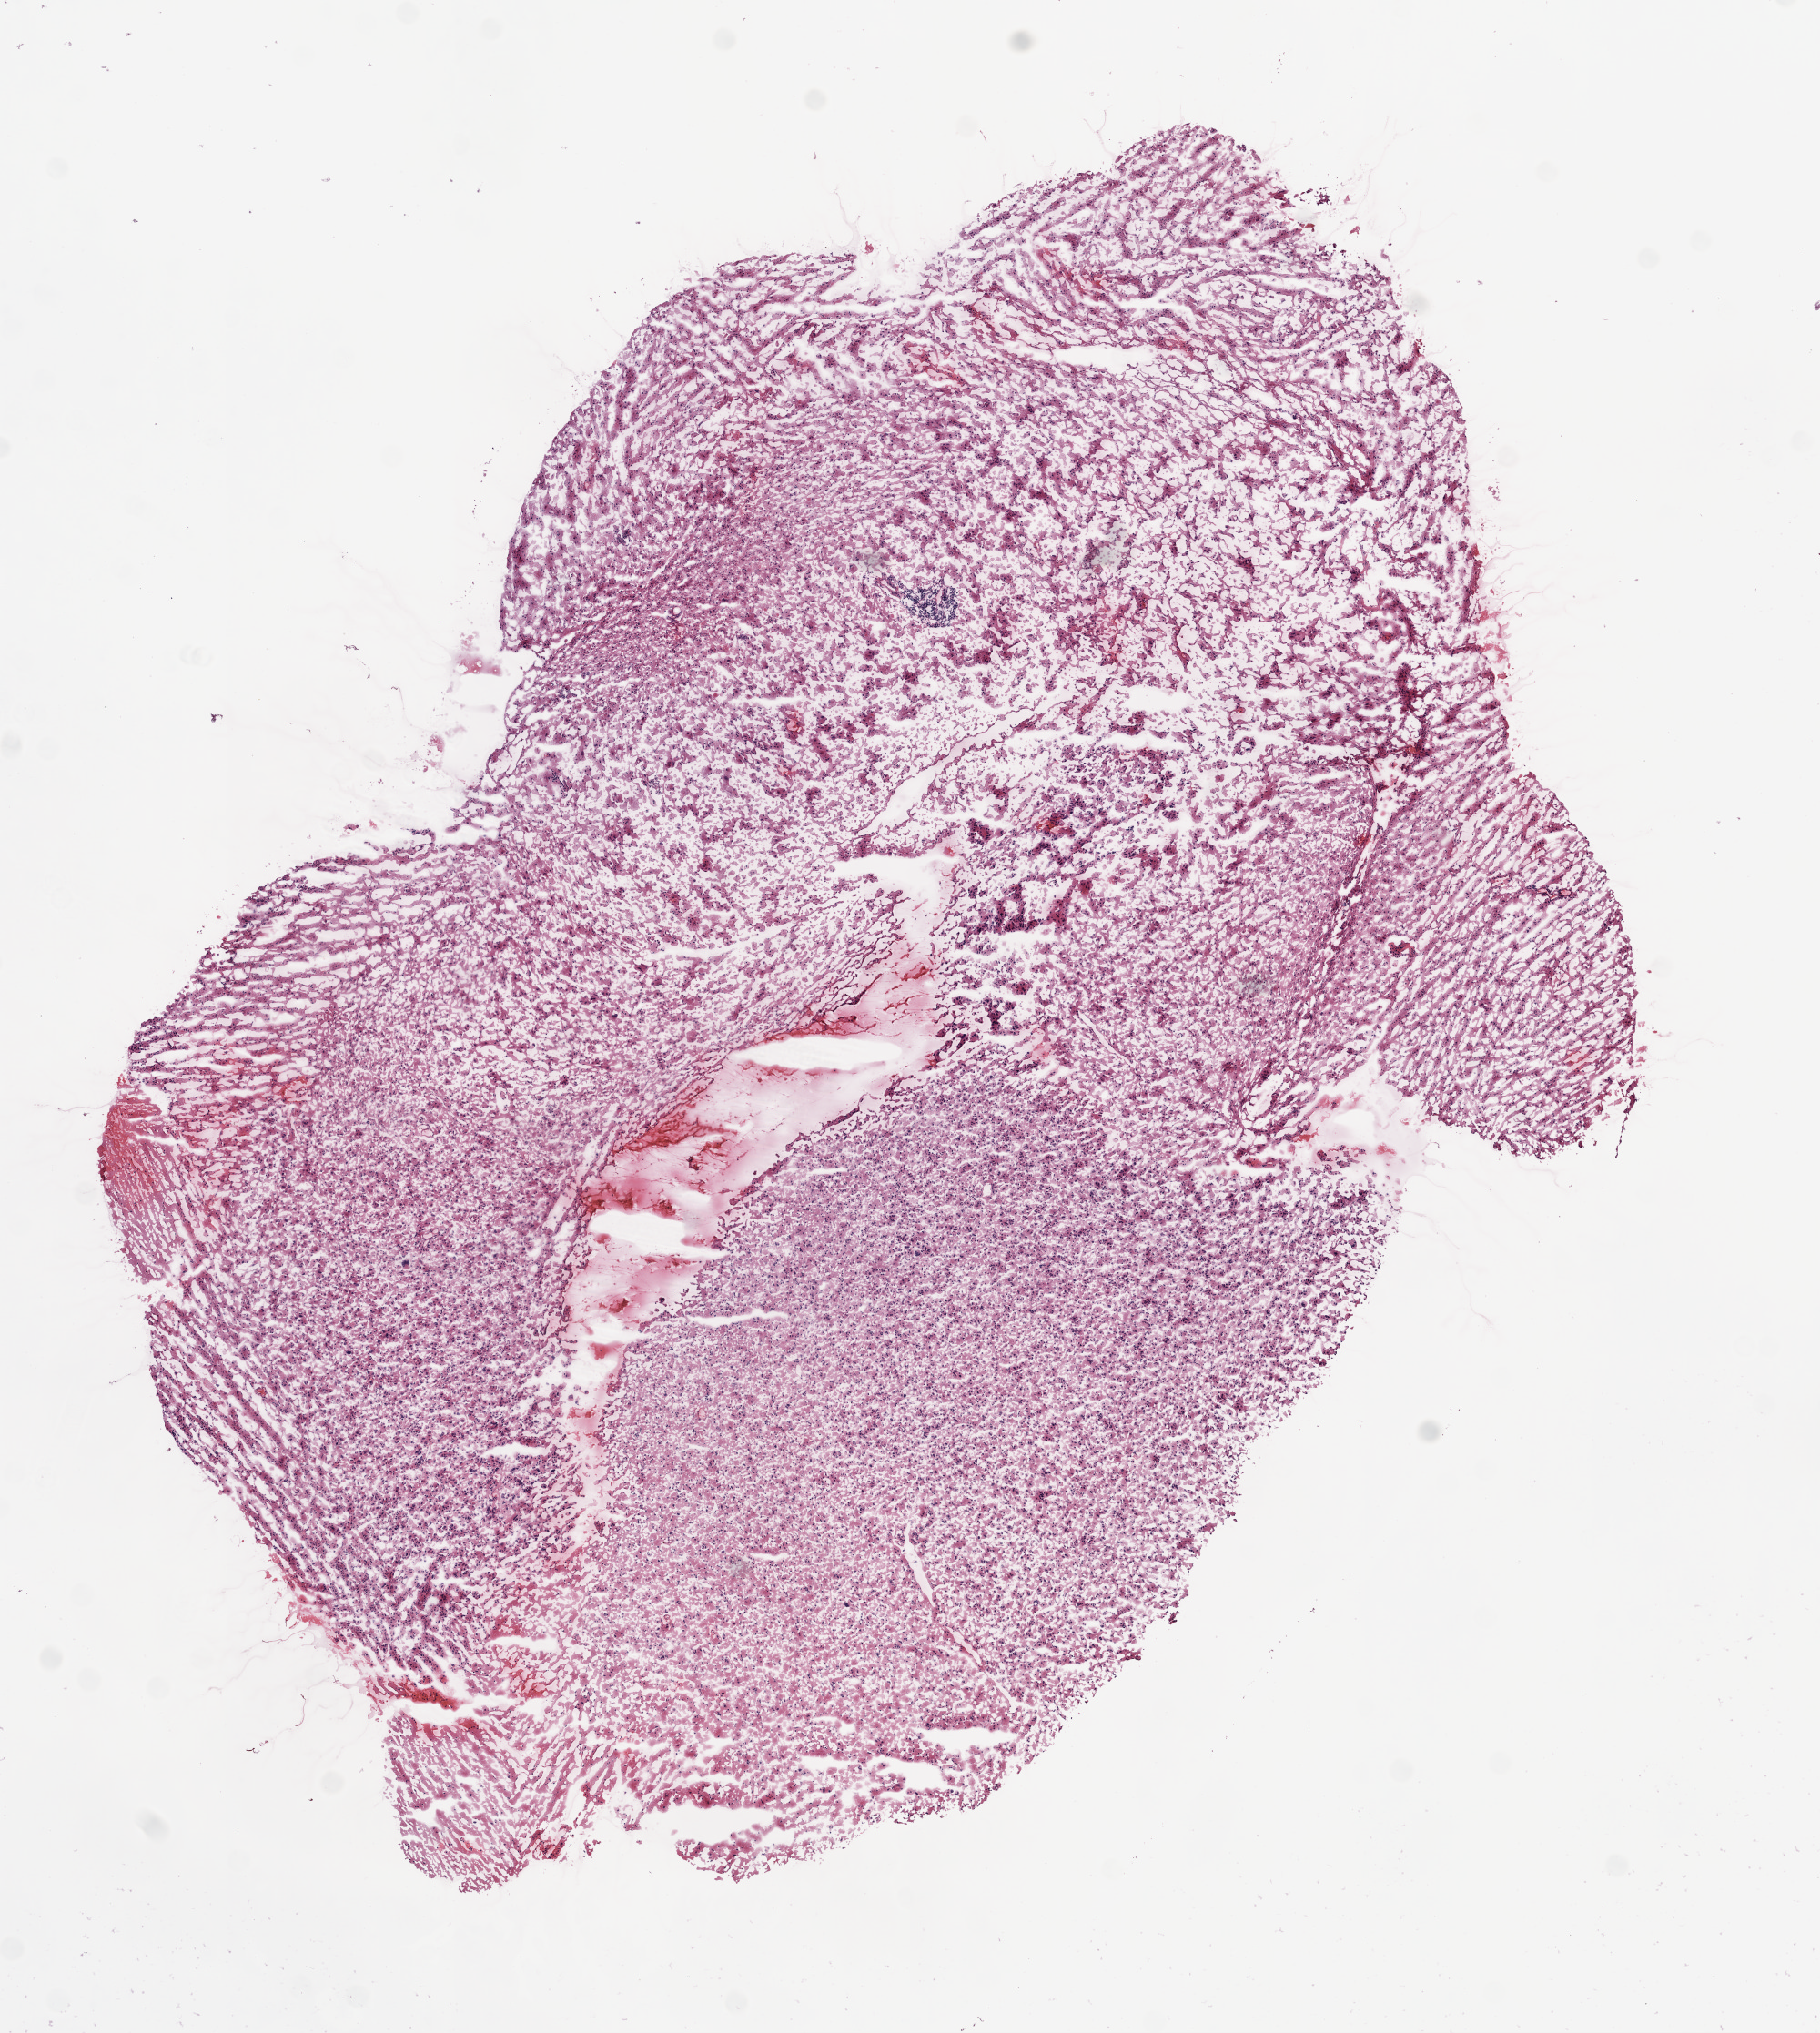
Whole-slide histology image, H&E-stained, shown as a low-resolution overview of the whole scanned area (about 8.0 x 9.0 mm); frozen section; primary tumour sample from the brain. Male, age 67 years at initial diagnosis. Histologic grade: G3 (poorly differentiated). Slide review estimates, as recorded: tumour cells 100%, tumour nuclei 75%, normal cells 0%, stromal cells 0%, necrosis 0%.
* diagnosis: Astrocytoma, anaplastic